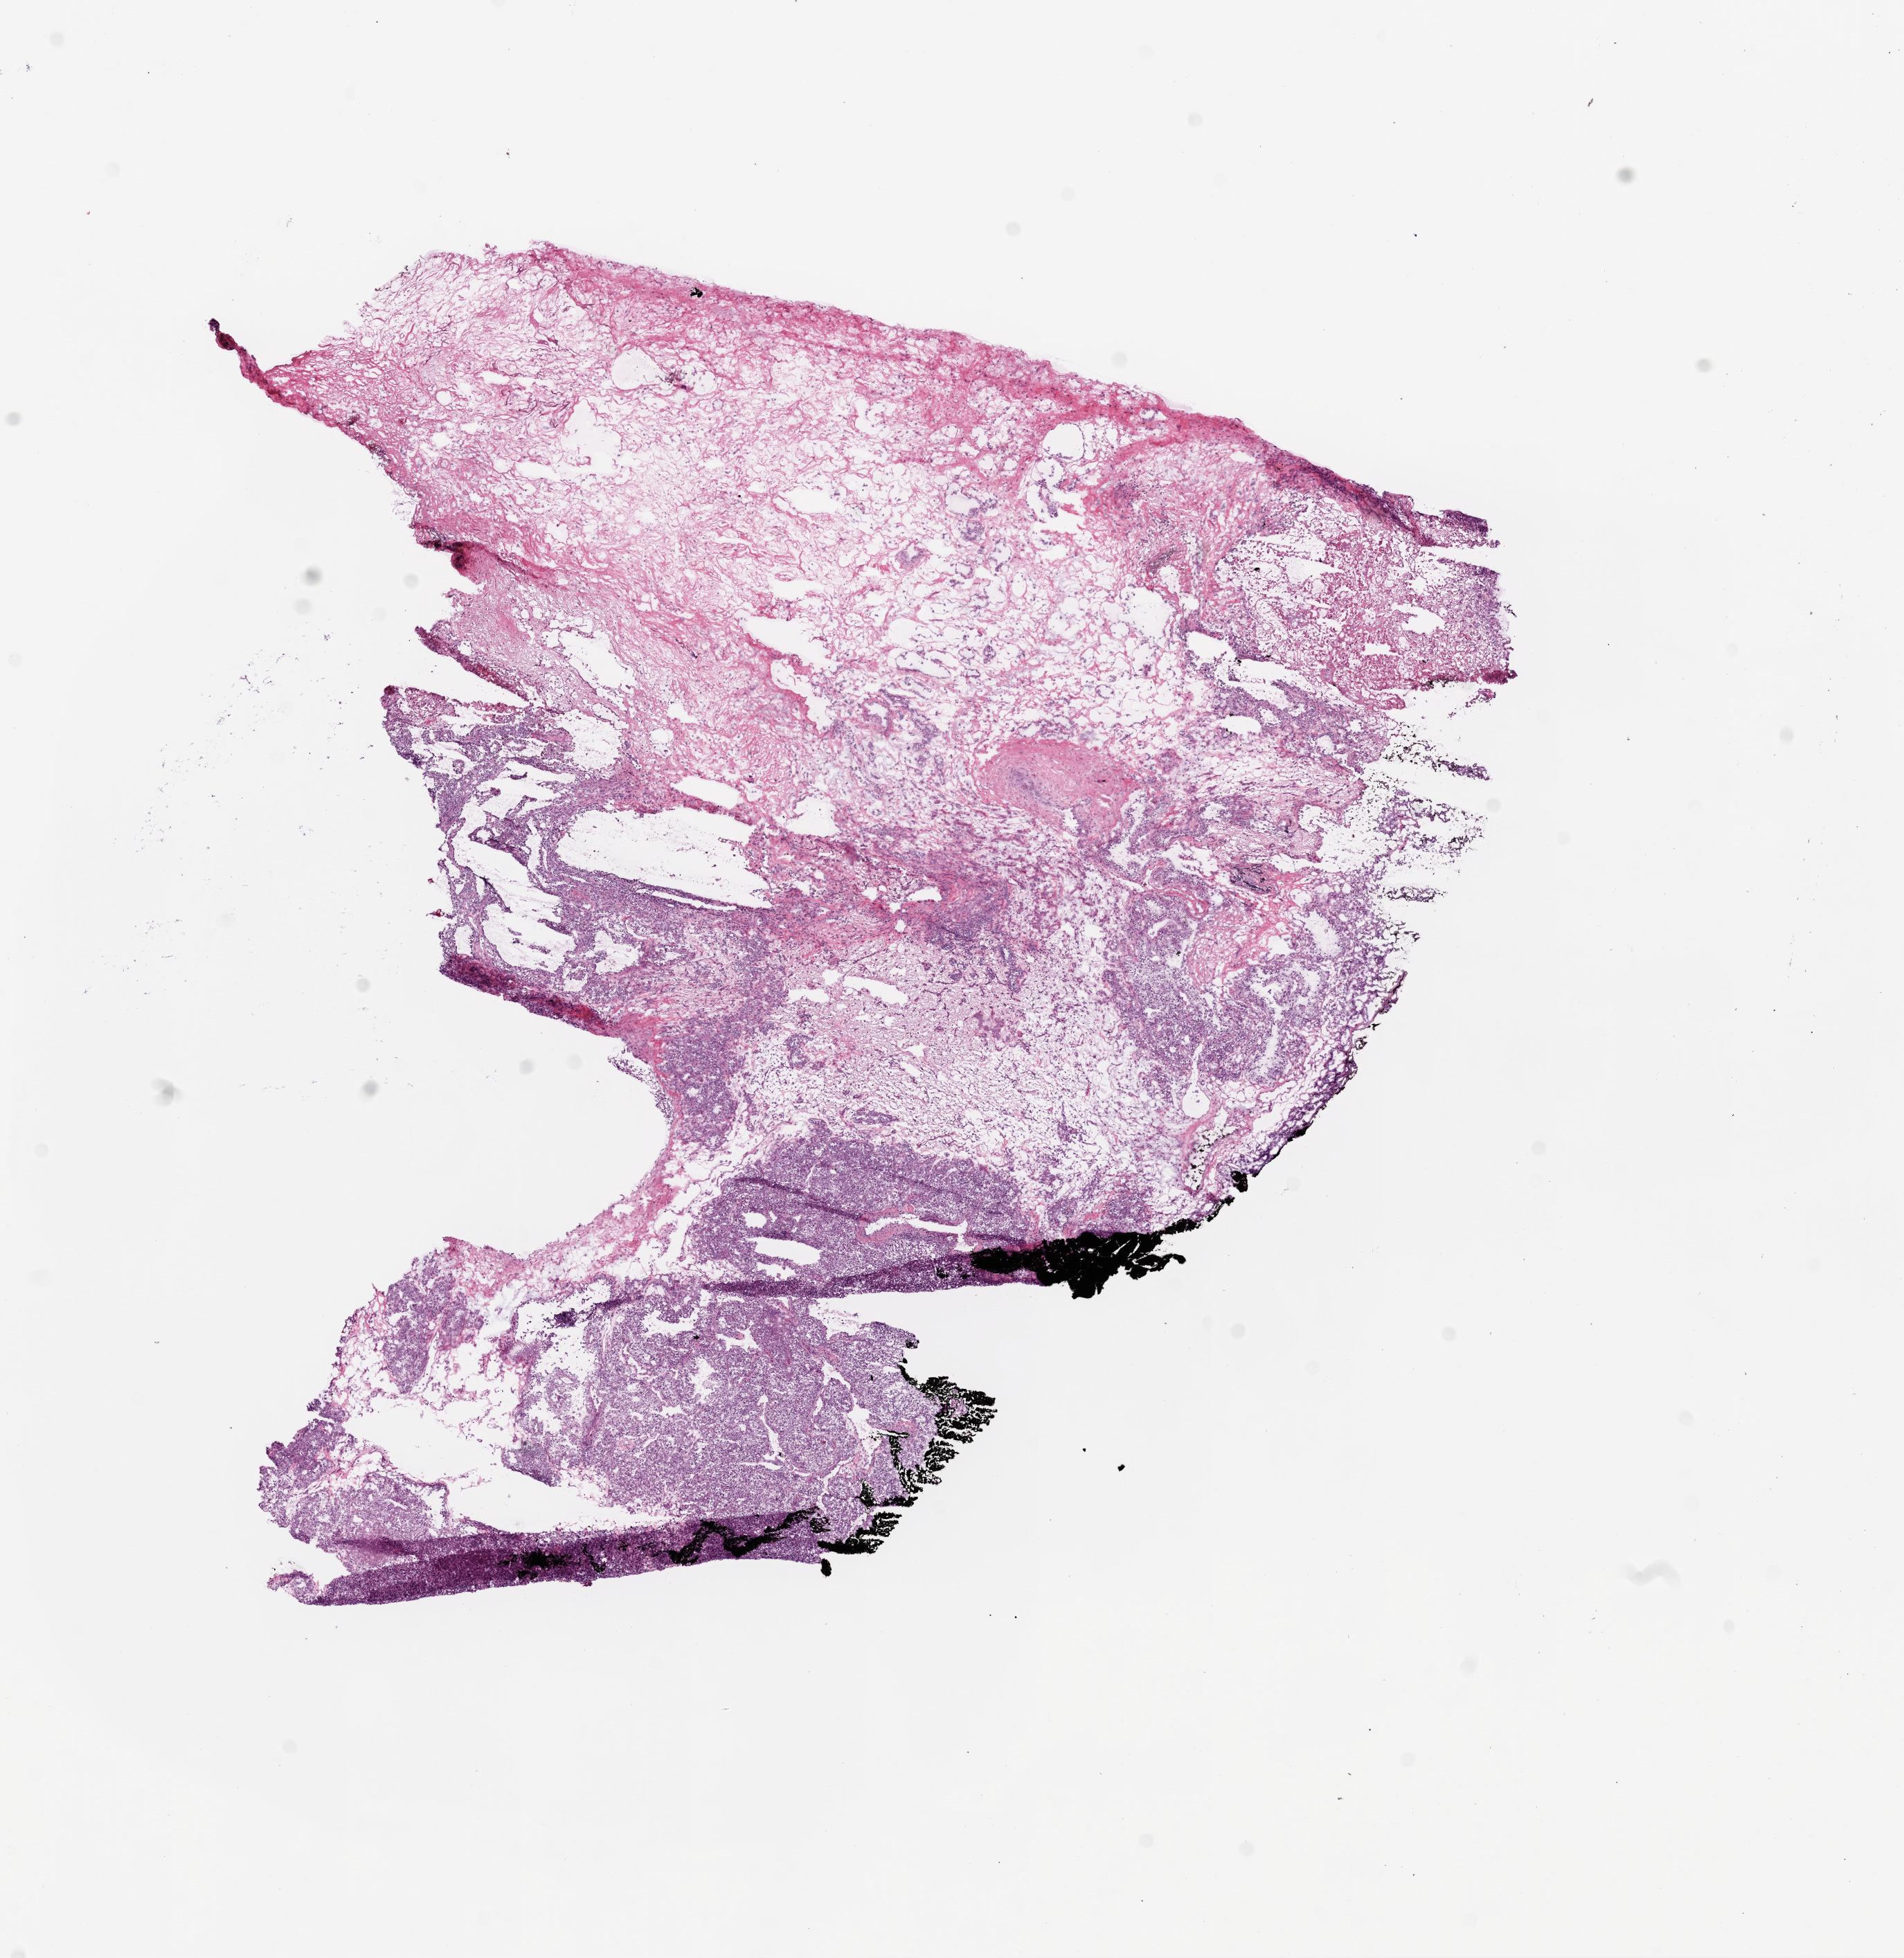
H&E whole-slide image — low-resolution overview of the scanned area, about 11.0 x 11.3 mm (from a 20x scan), frozen section from the top of the tissue portion, sample: primary tumour, kidney. Patient: male, age at initial diagnosis 51 years. Histologic grade: G3 (poorly differentiated). Composition of this section per pathologist review: tumour cells 30%, tumour nuclei 85%, normal cells 55%, stromal cells 5%, necrosis 10%.
Laterality: right. AJCC pathologic stage: I. Pathologic diagnosis: Clear cell adenocarcinoma, NOS.